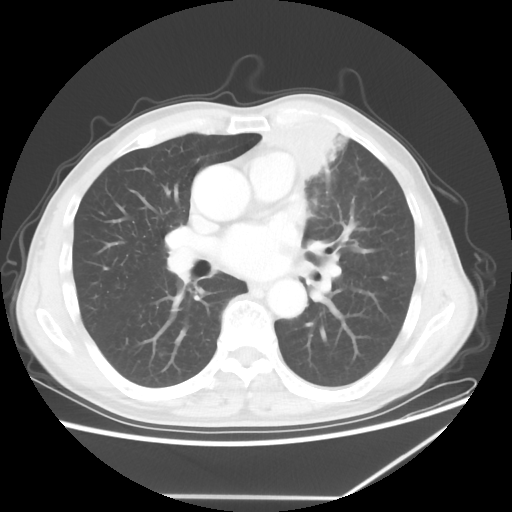
Chest CT, one axial slice; slice 33 of 64 in the series (ordered by position); reconstruction kernel STANDARD; lung window (W 1500 / L -600 HU); 5 mm slice thickness; 512 × 512 image matrix, field of view 383 × 383 mm. Male patient, age 64 years. Case-level facts recorded for this patient, not image findings: clinical TNM (as recorded): T1c N1 M1; histopathological grade: G2.
Annotated regions visible in this slice (bounding box drawn by a radiologist):
- lung tumour (recorded histology: squamous cell carcinoma): bounding box (x1, y1, x2, y2) in pixels: (260, 118, 370, 209)